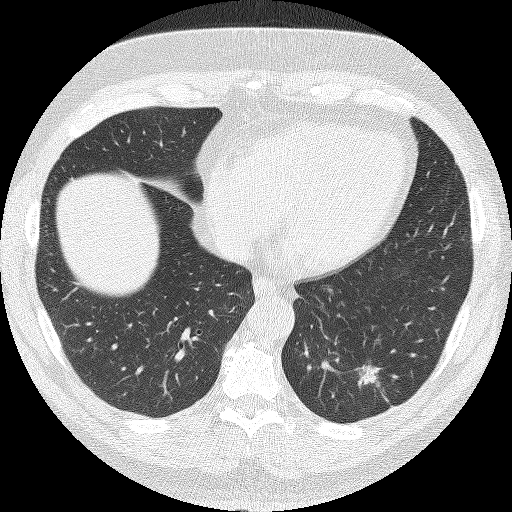
Low-dose screening chest CT, one axial slice. Position 42 of 140 along the scan axis. Reconstruction kernel FC51. 120 kVp. Lung window (W 1500 / L -600 HU). 2 mm slice thickness. 512 × 512 image matrix, field of view 349 × 349 mm.
Annotated regions visible in this slice (manually delineated by an expert):
- lesion 1 (tumor, lower lobe of left lung): bounding box <354,365,381,388> (left, top, right, bottom; pixels)